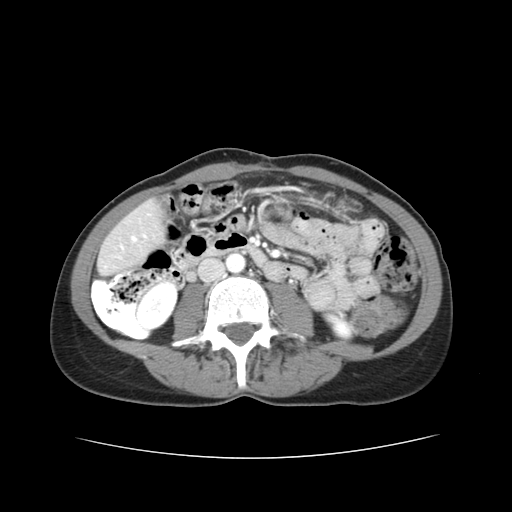
Contrast-enhanced abdominal CT, one axial slice; position 7 of 38 along the scan axis; reconstruction kernel STANDARD; intravenous contrast given; soft-tissue window (W 400 / L 40 HU); 512 × 512 image matrix, field of view 340 × 340 mm. Female patient, age 54 years. Case-level facts recorded for this patient, not image findings: diagnosis: colorectal cancer liver metastases, imaged before liver resection; multiple liver metastases: yes; largest metastasis: 1.1 cm; disease in both lobes: yes.
Outlined on this slice (expert manual segmentation):
- hepatic veins: box from (x=132, y=238) to (x=136, y=241) px
- liver: (x=101, y=204)–(x=164, y=271)